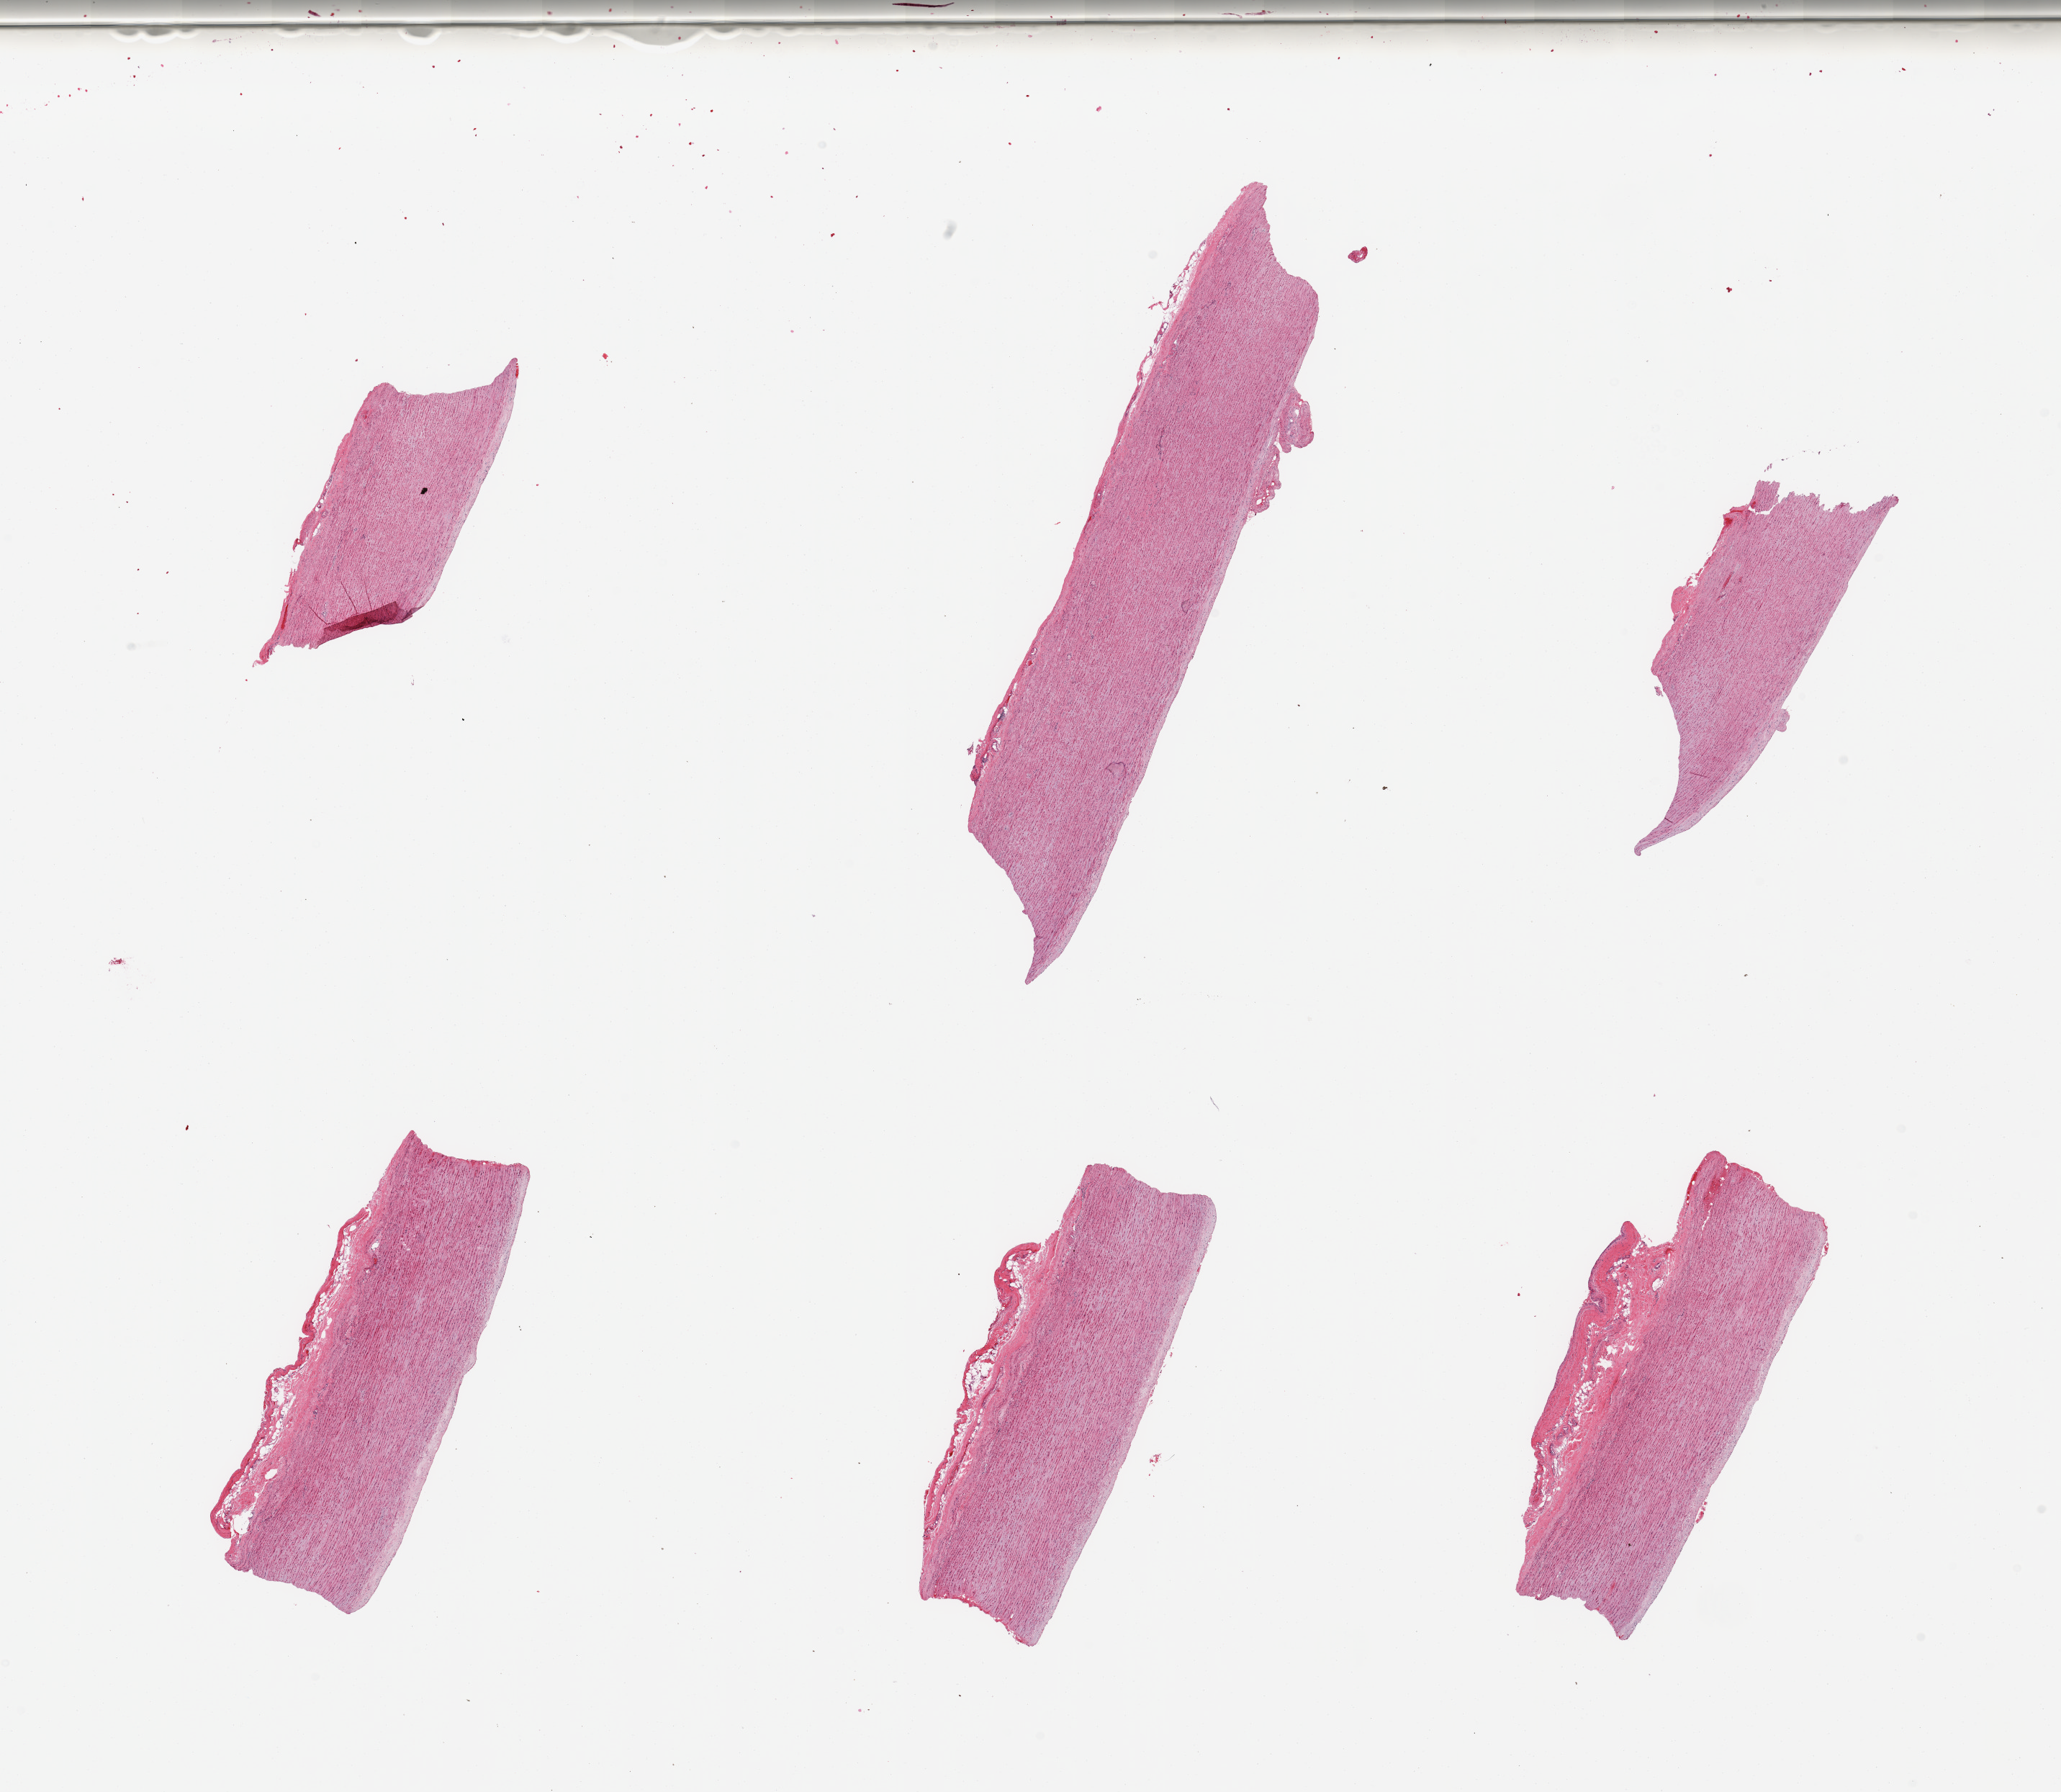
Digitized haematoxylin and eosin-stained section — whole scanned area (about 22.6 x 19.7 mm, from a 20x scan) shown as a low-resolution overview. PAXgene-fixed, paraffin-embedded tissue. Target tissue: aorta. Donor tissue sample.
• pathologist's review note for this sample: 6 pieces; mild plaque